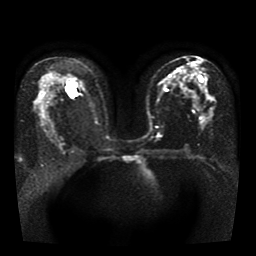
Breast MRI, one axial slice. Slice 22 of 41 in the series (ordered by position). Diffusion-weighted series; image 2 of 4 stored at this slice position (different b-values; order by instance number). 1.5 T. 5 mm slice thickness. 256 × 256 image matrix. Female patient.
Structures marked on this image (manually delineated by an expert):
- tumour on diffusion-weighted imaging: bounding box <68,84,76,96> (left, top, right, bottom; pixels)